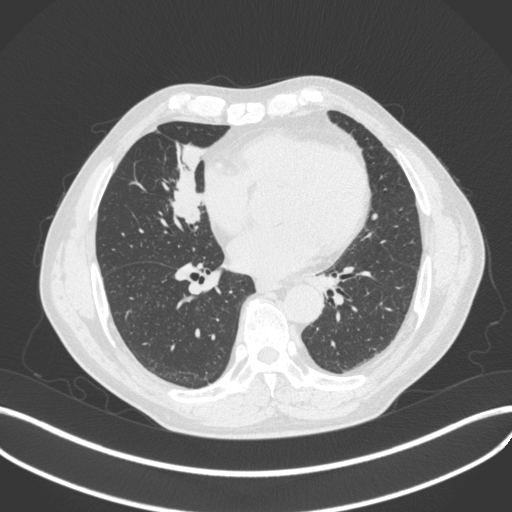
Chest CT, one axial slice. Position 168 of 429 along the scan axis. Reconstruction kernel B31f. Lung window (W 1500 / L -600 HU). 1 mm slice thickness. 512 × 512 image matrix, field of view 400 × 400 mm. Male patient, age 61 years. Case-level facts recorded for this patient, not image findings: clinical TNM (as recorded): T2b N1 M0.
Outlined on this slice (bounding box drawn by a radiologist):
- lung tumour (recorded histology: squamous cell carcinoma): box from (x=162, y=140) to (x=208, y=228) px